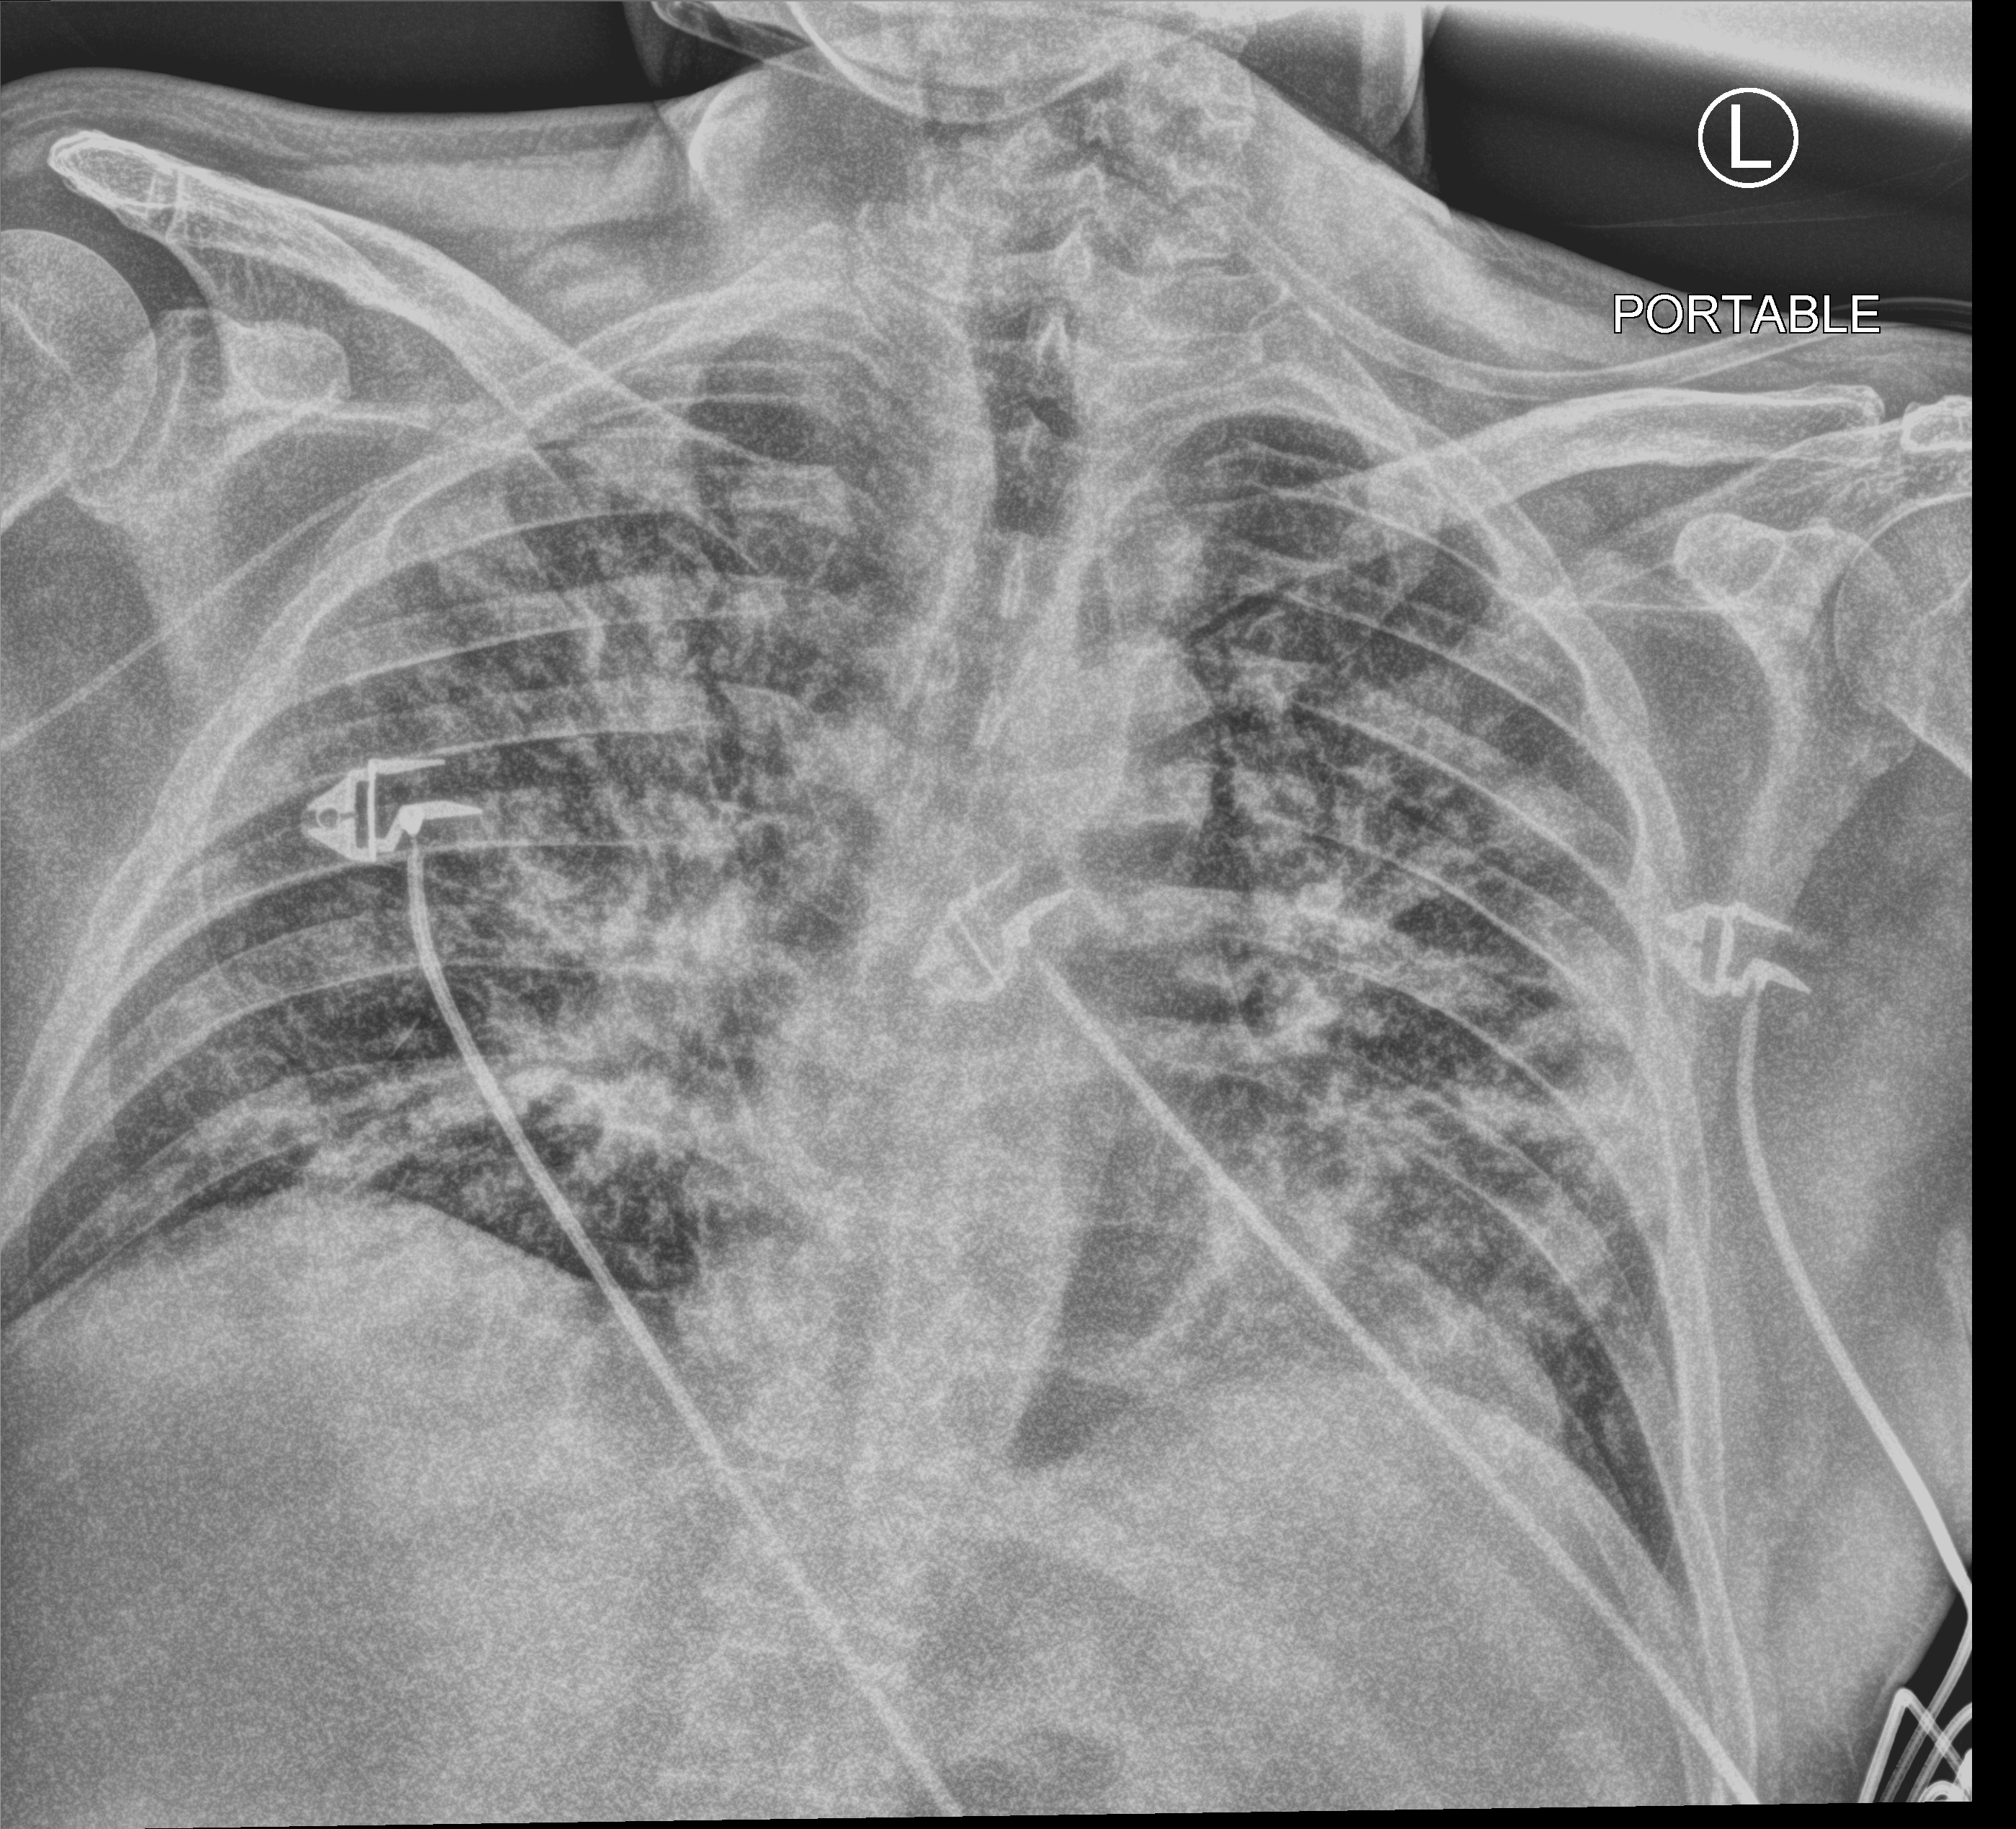
Portable chest radiograph; anteroposterior (AP) projection. Male patient hospitalised with COVID-19, age 60–74 years.
From the hospital-stay record, not from the radiograph (when in the stay this image was taken is not recorded): smoking status (admission record): never; length of hospital stay: 24 days; diabetes (admission record): yes.